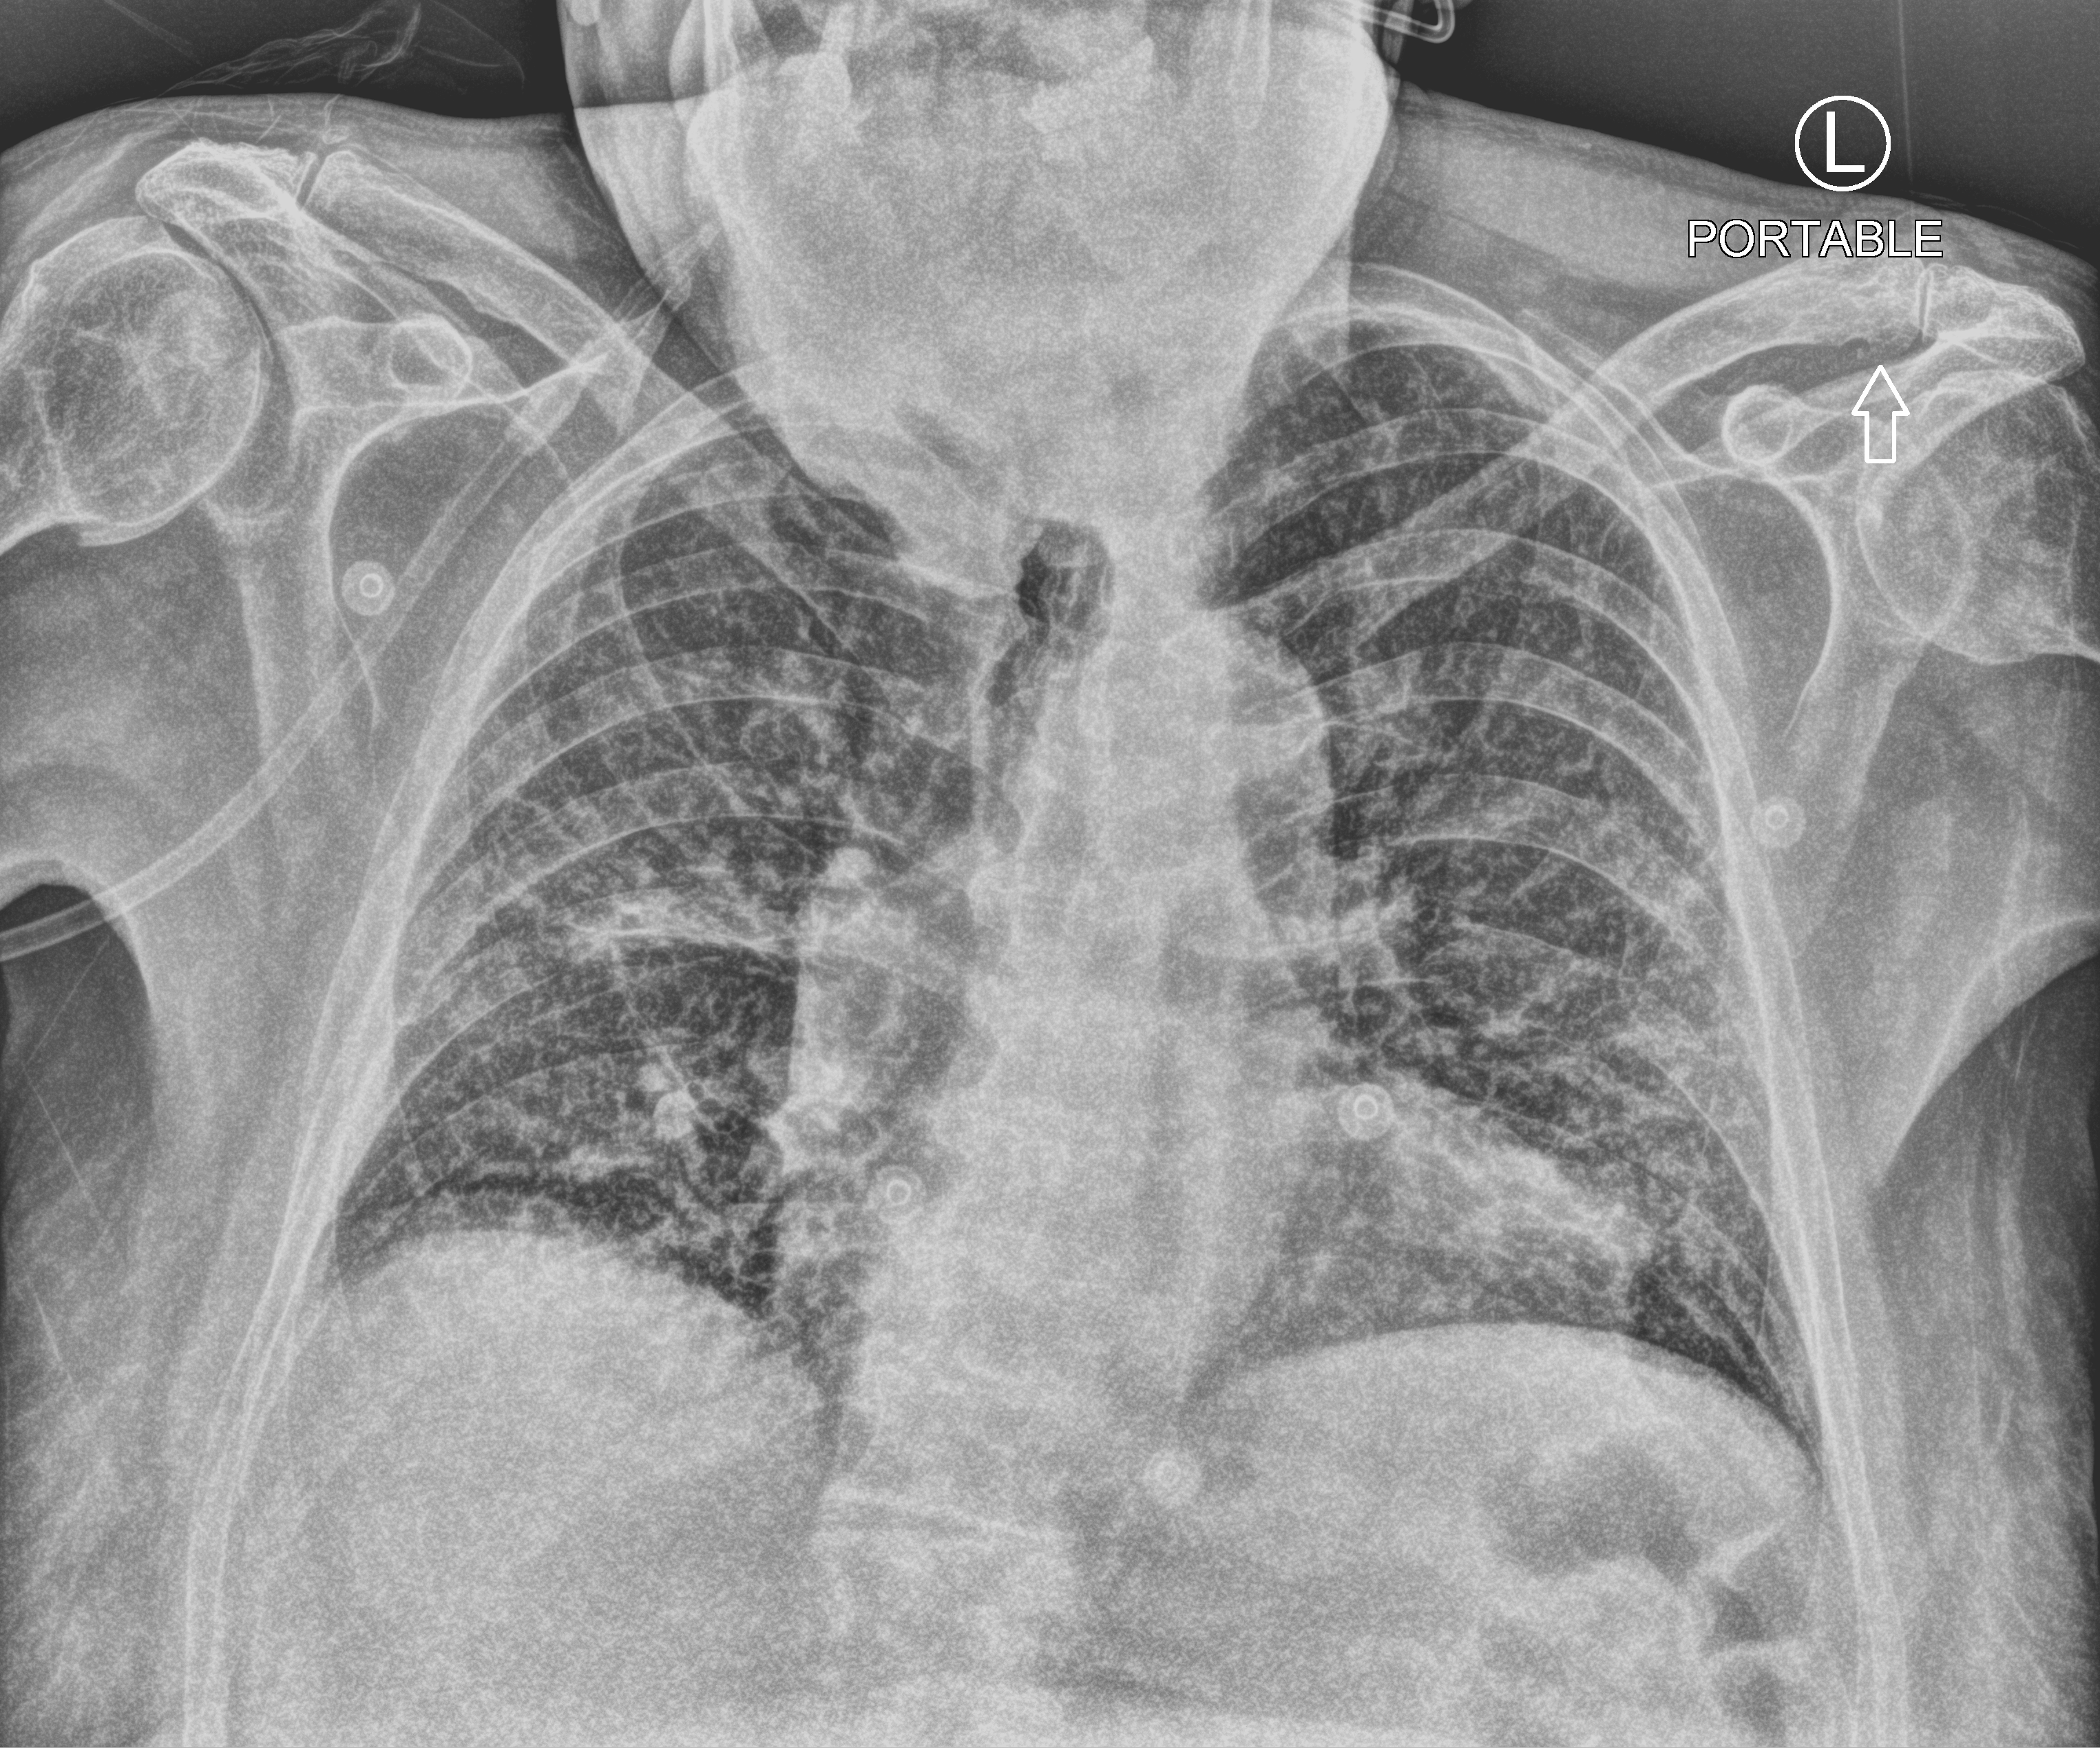
Chest X-ray (portable); anteroposterior (AP) projection. Male patient hospitalised with COVID-19, age 75–90 years.
From the hospital-stay record, not from the radiograph (when in the stay this image was taken is not recorded): admitted to intensive care during this hospital stay: no; mechanically ventilated during this hospital stay: no.